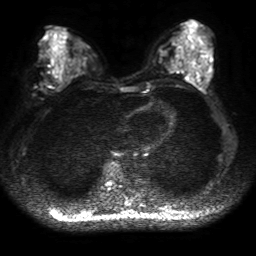
Breast MRI, one axial slice; slice 24 of 50 in the series (ordered by position); diffusion-weighted series; image 2 of 4 stored at this slice position (different b-values; order by instance number); 1.5 T; 4 mm slice thickness; 256 × 256 image matrix, field of view 320 × 320 mm. Female patient.
Annotated regions visible in this slice (manually delineated by an expert):
- tumour on diffusion-weighted imaging: bounding box [x1, y1, x2, y2] px = [45, 82, 52, 86]